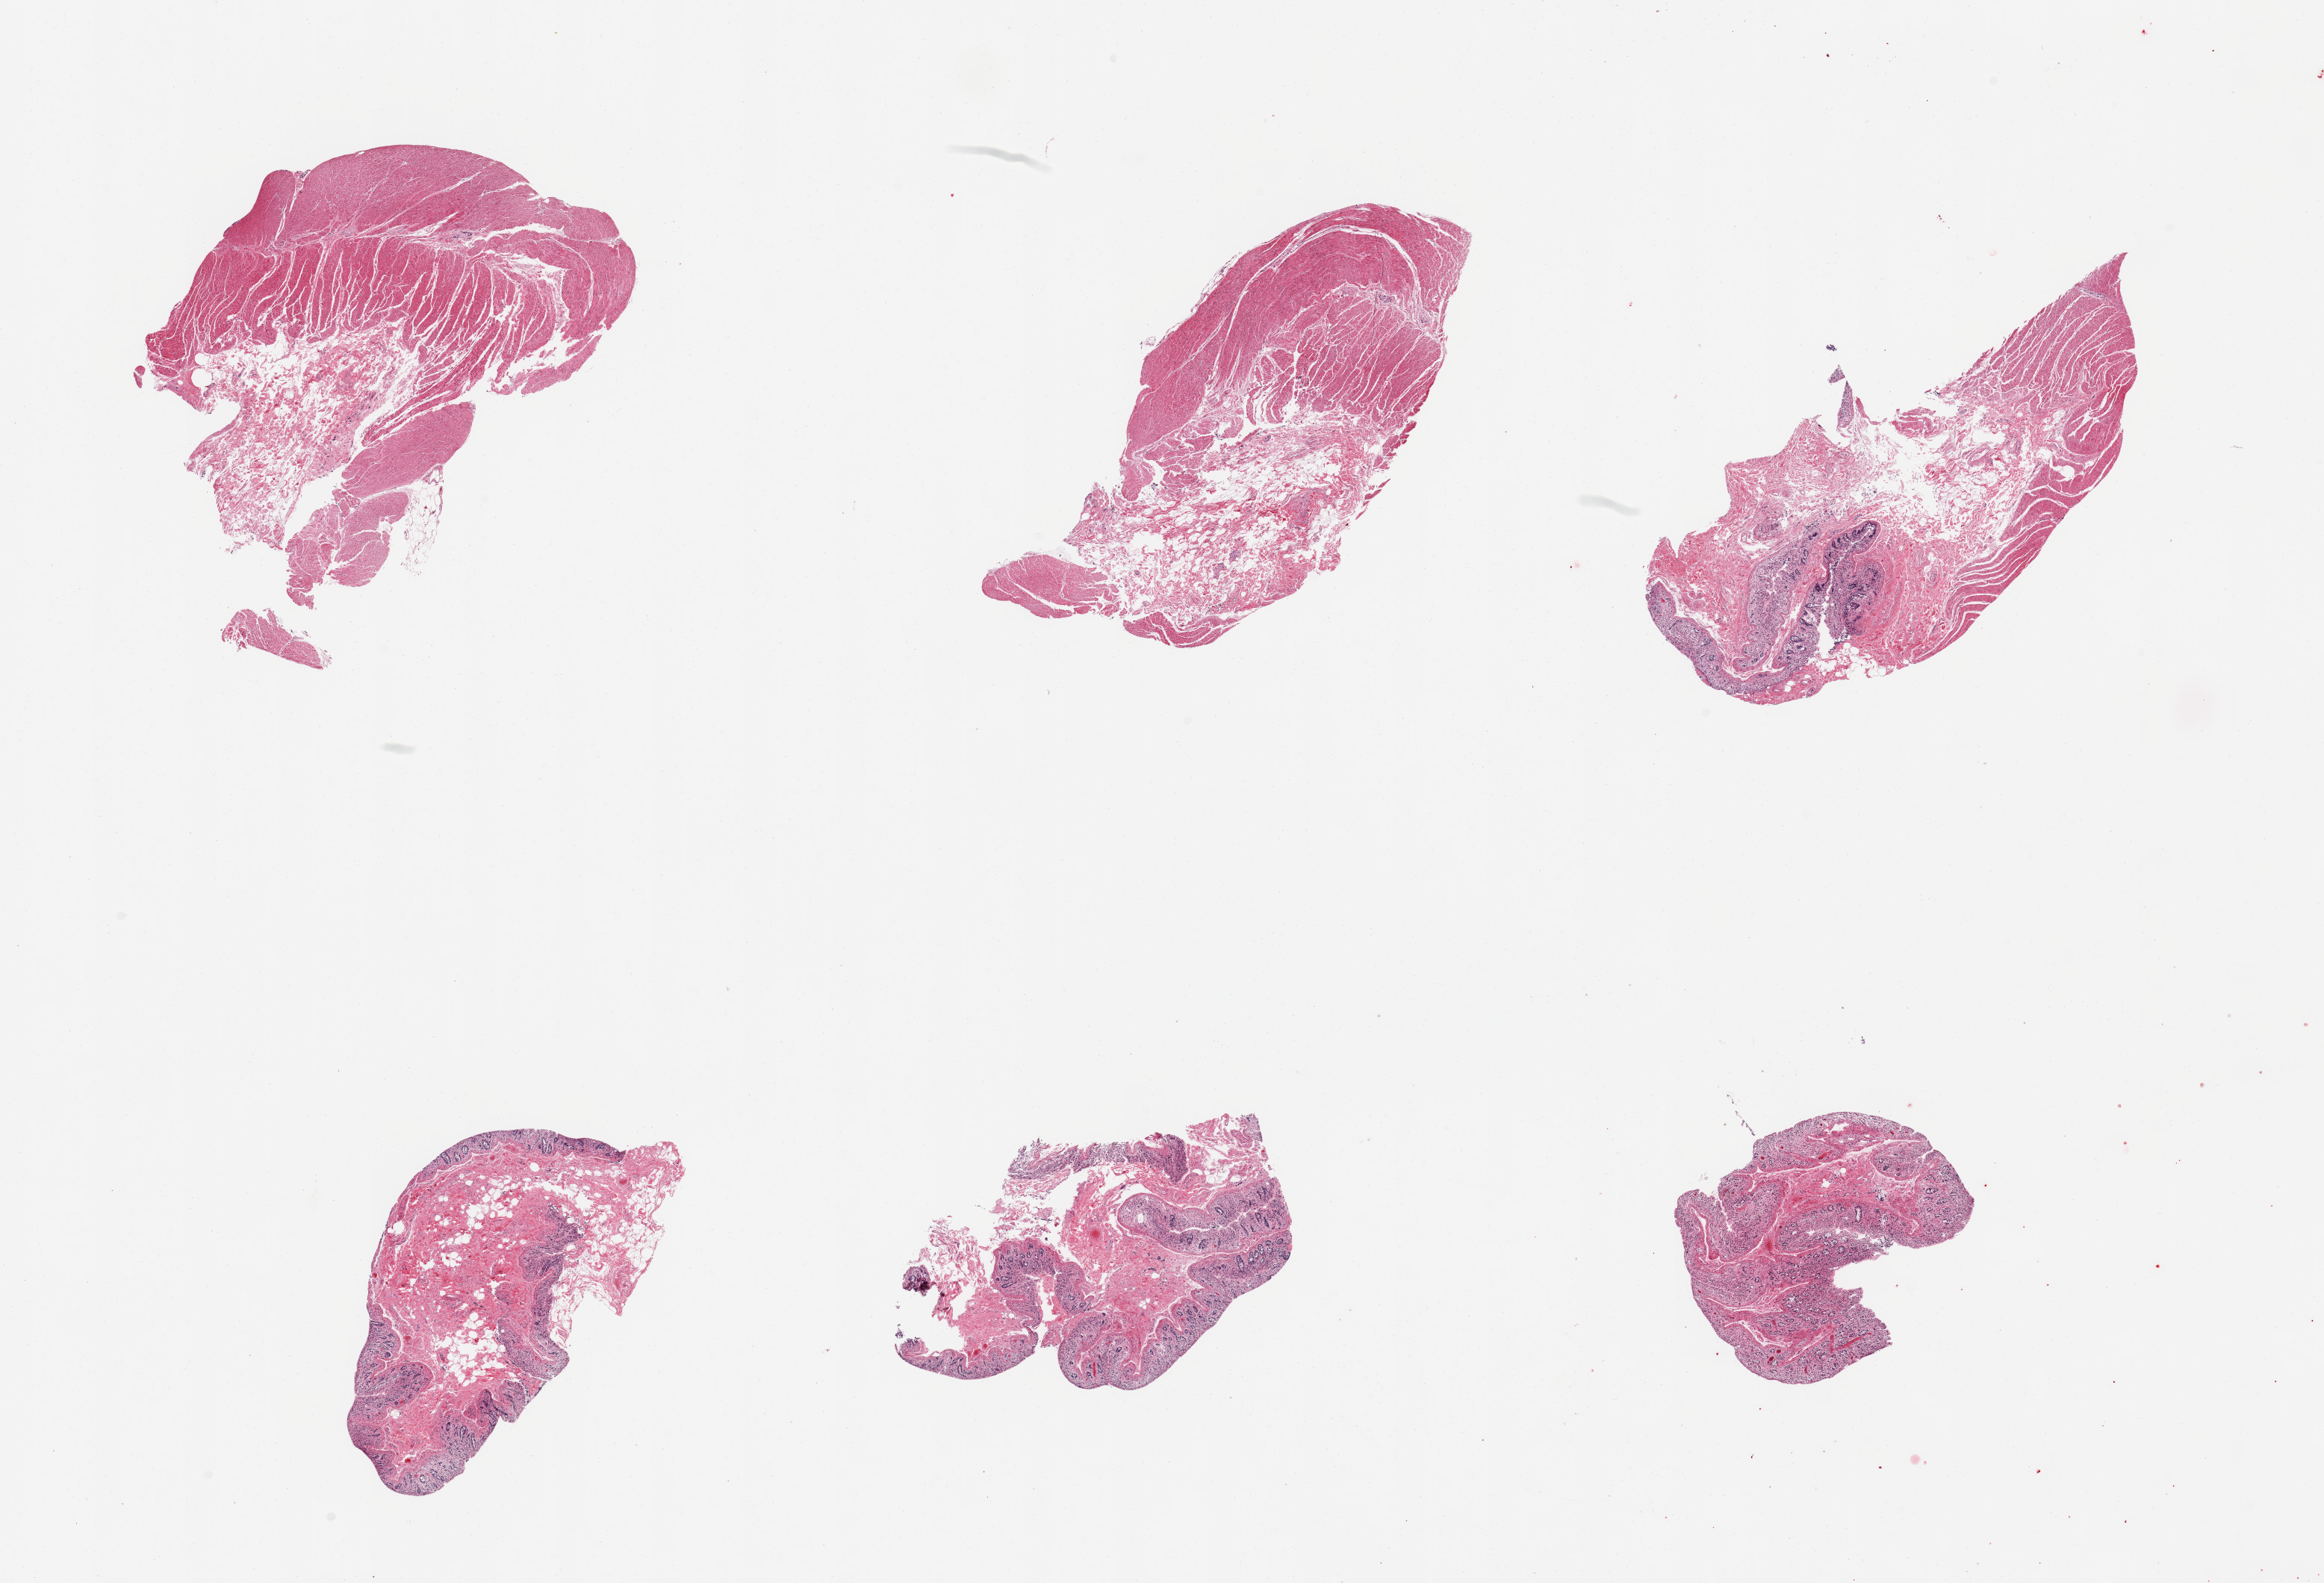
H&E whole-slide image, low-resolution overview of the scanned area, about 24.6 x 16.8 mm (from a 20x scan), PAXgene-fixed paraffin-embedded (PFPE) section, target tissue: sigmoid colon, donor tissue sample. Donor sex: male.
* pathologist's review note for this sample: 6 pieces; variable representation of muscularis and autolyzed colonic mucosa